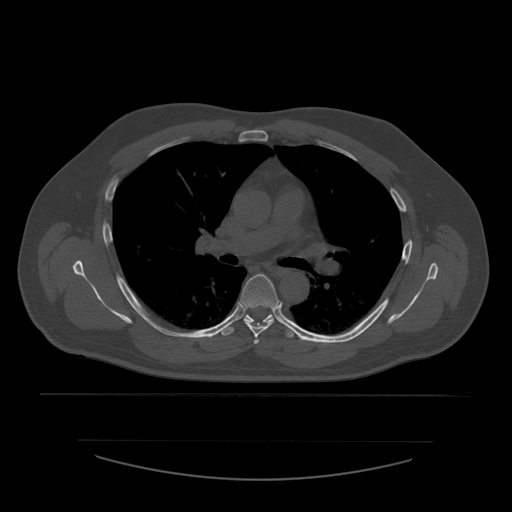
CT including the spine, one axial slice. Position 391 of 532 along the scan axis. Reconstruction kernel STANDARD. 120 kVp. Bone window (W 1800 / L 400 HU). 1.25 mm slice thickness. 512 × 512 image matrix, field of view 441 × 441 mm. Patient age 44 years. From the clinical record (not read from this slice): primary cancer: soft tissue sarcoma.
Structures marked on this image (semi-automatically segmented with operator editing):
- T4 vertebra: bounding box <254,339,259,344> (left, top, right, bottom; pixels)
- T5 vertebra: <241,274,279,338>
- T6 vertebra: <220,314,296,338>